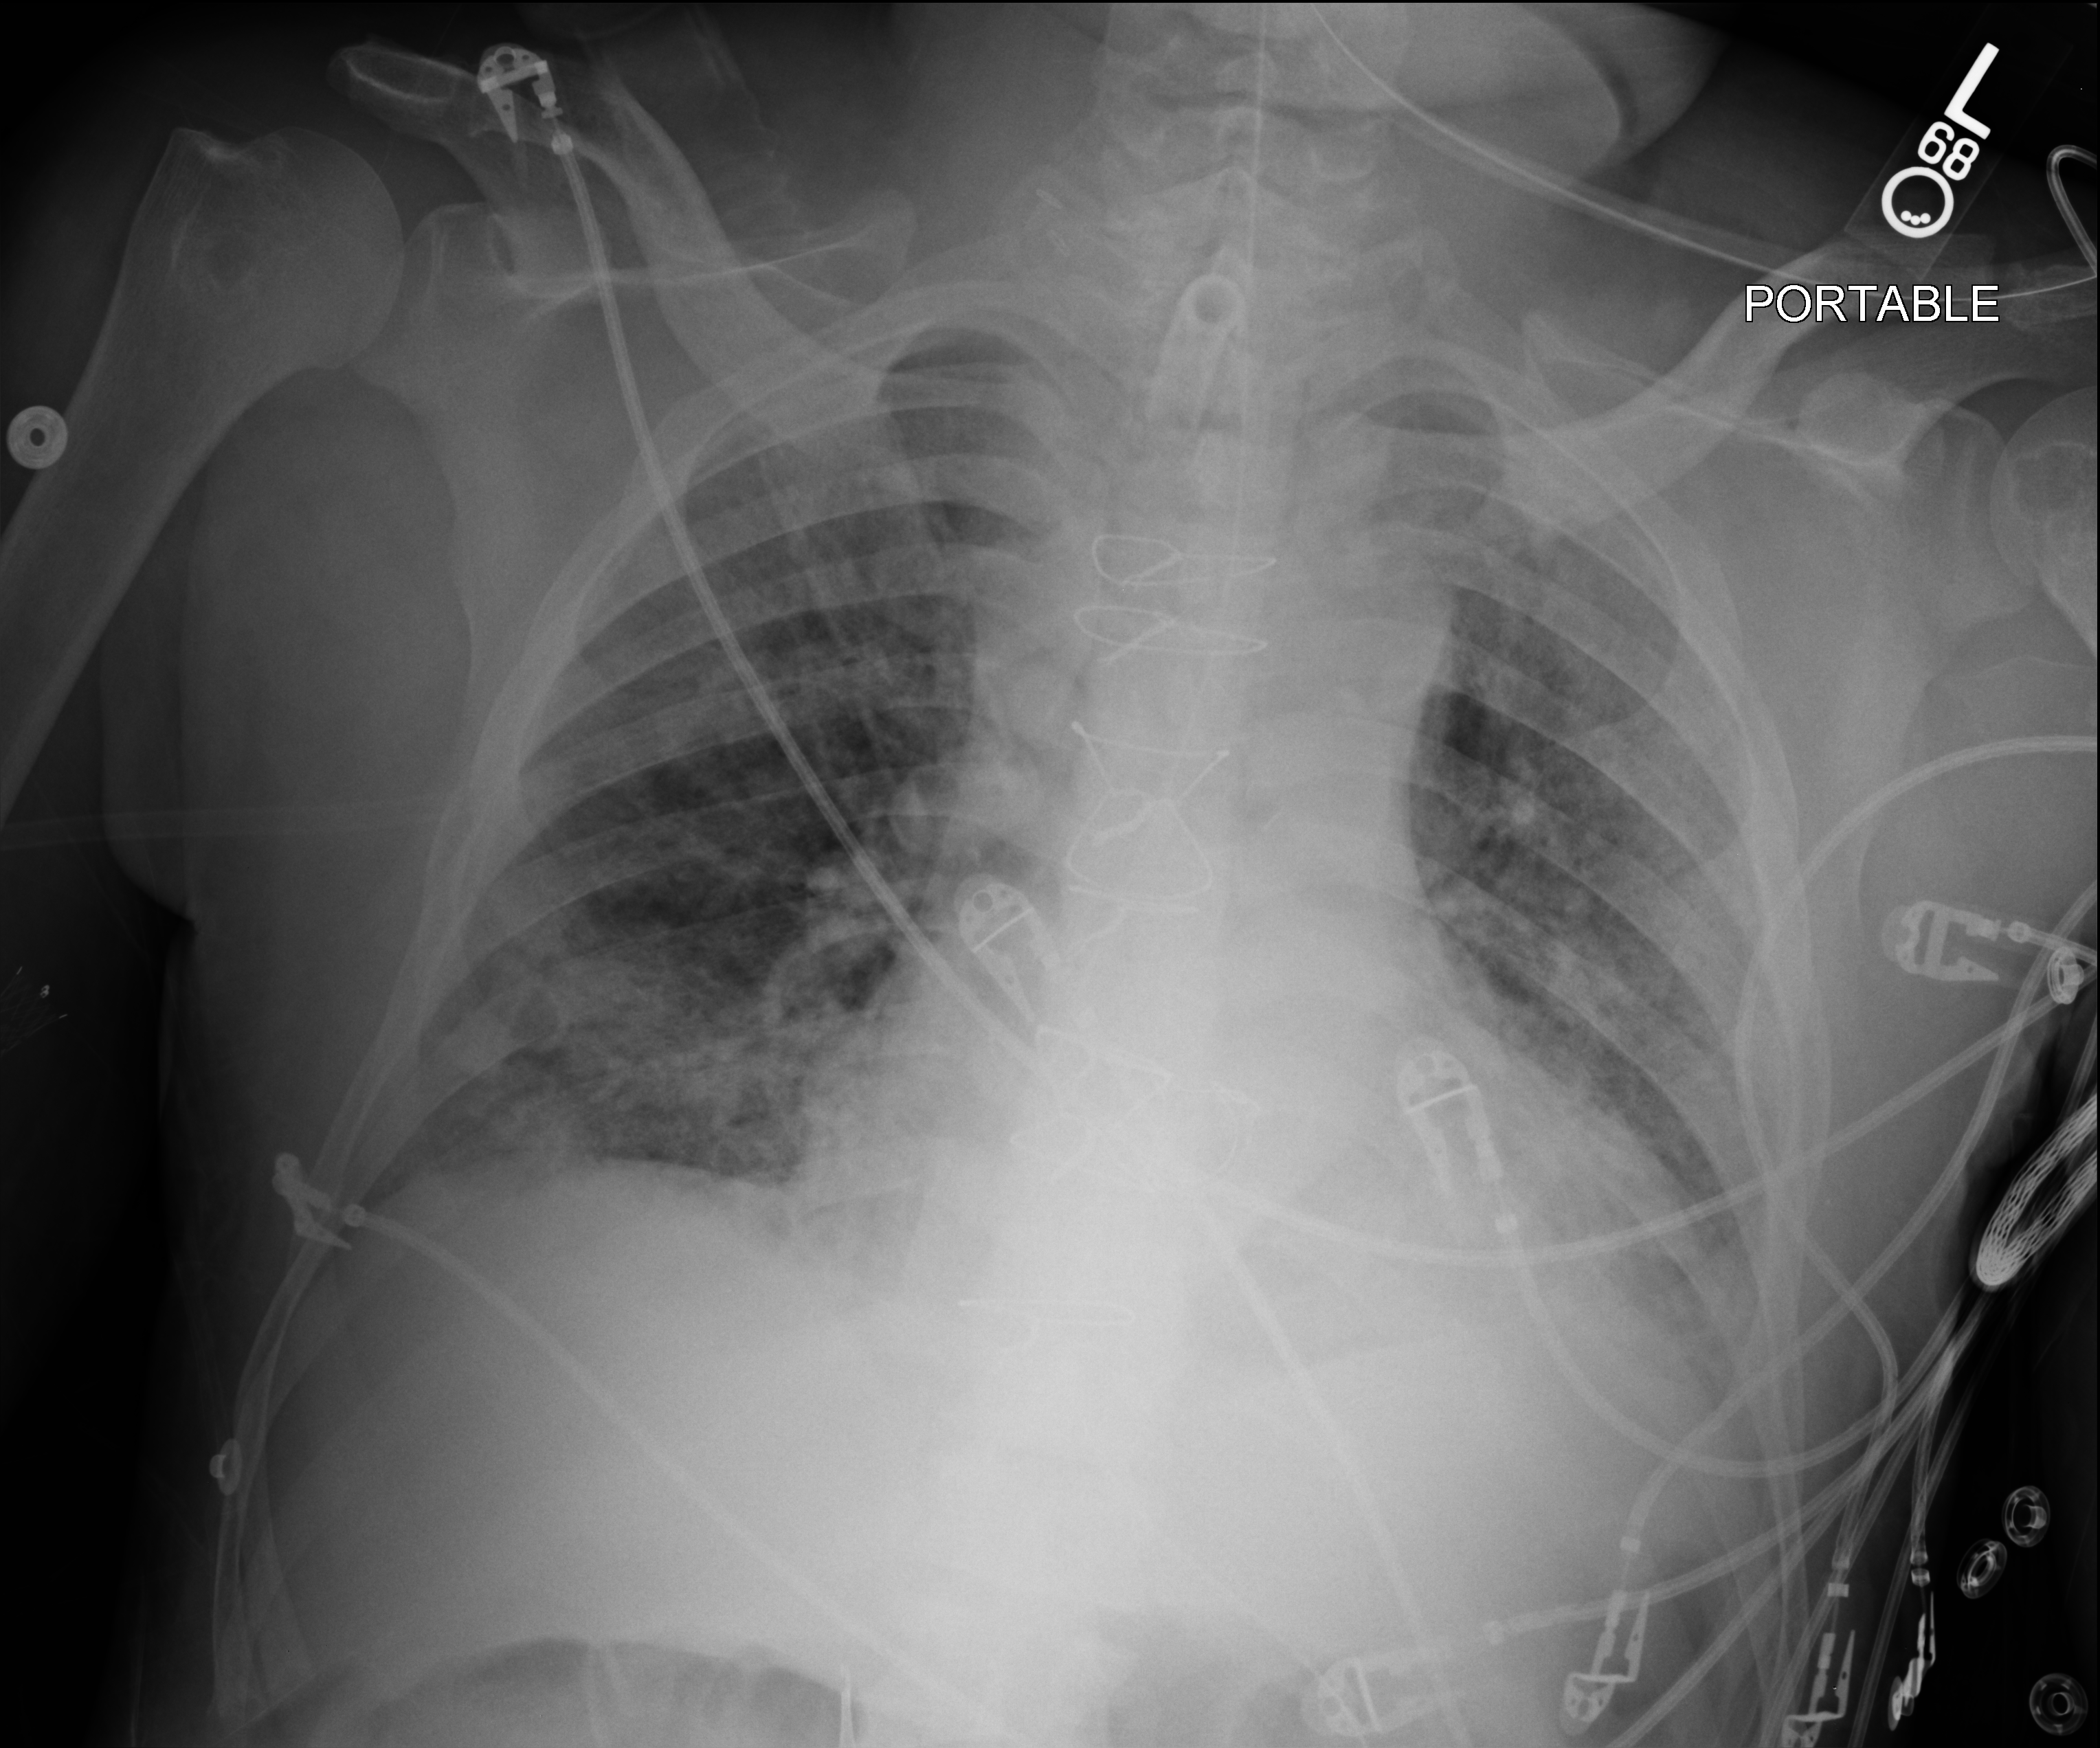
Chest X-ray (portable), anteroposterior (AP) projection. Male patient hospitalised with COVID-19, age 60–74 years.
From the hospital-stay record, not from the radiograph (when in the stay this image was taken is not recorded): length of hospital stay: 50 days; other chronic lung disease (admission record): no; smoking status (admission record): never.